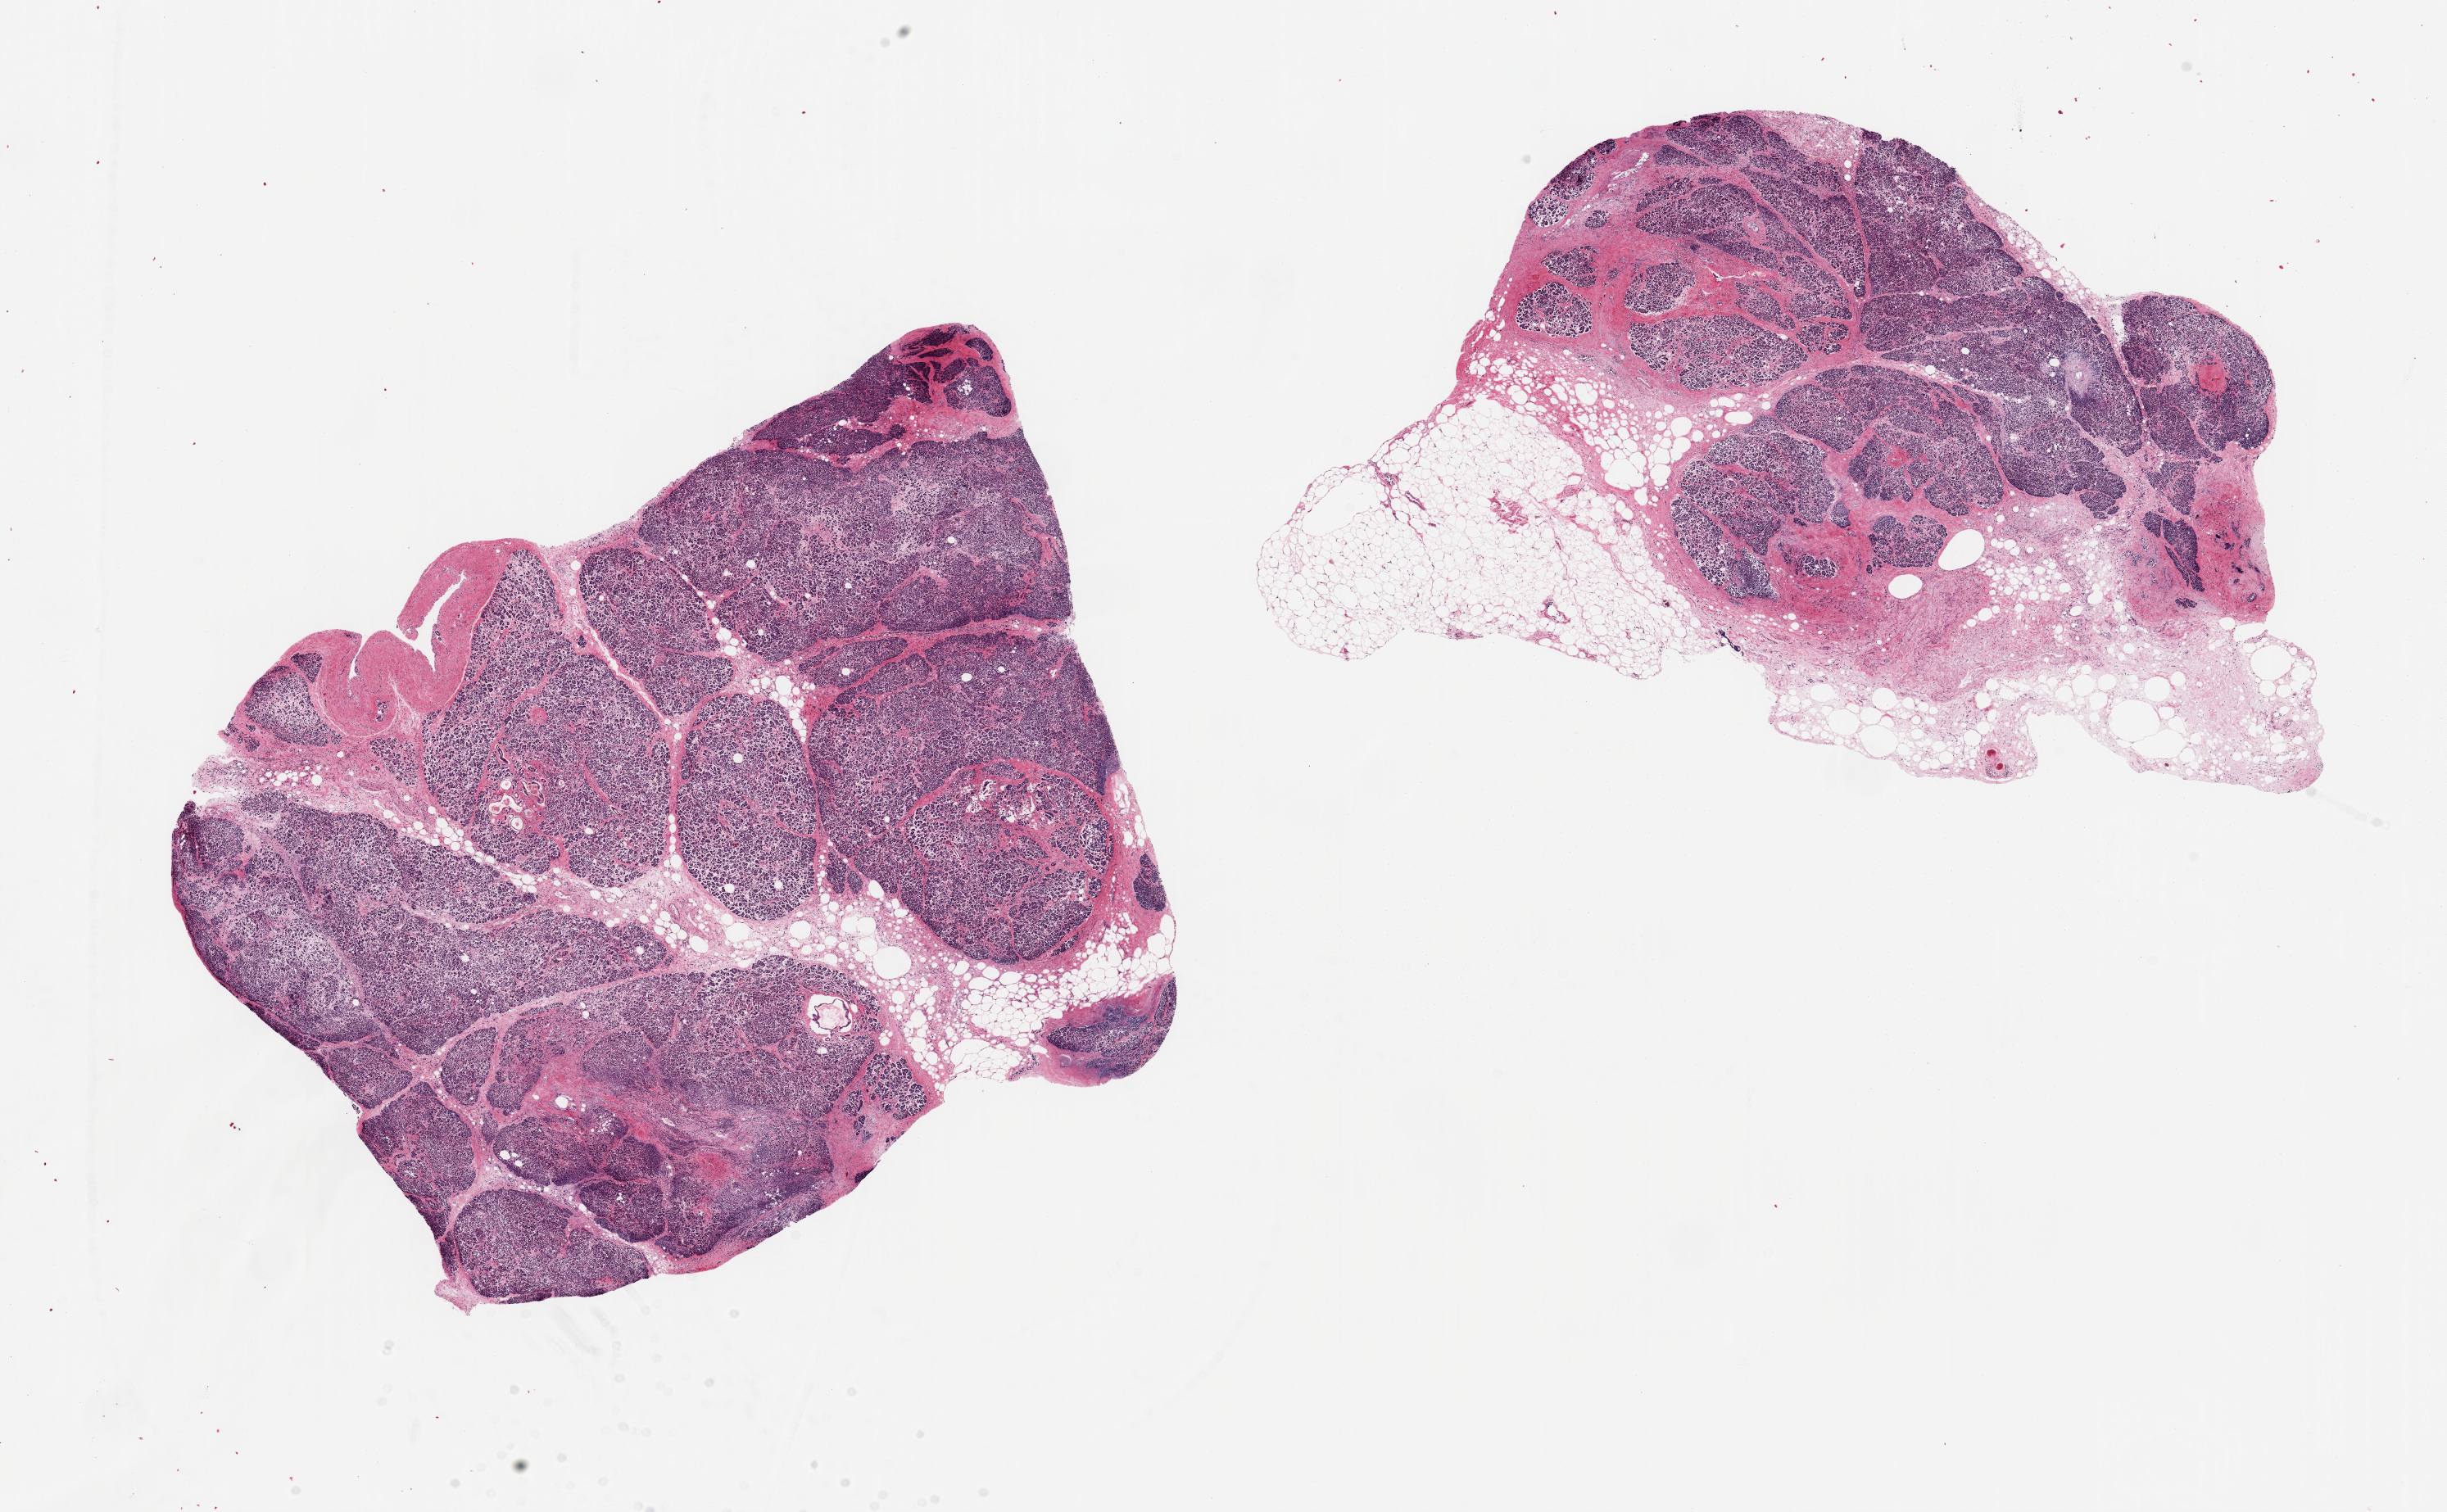
Haematoxylin and eosin whole-slide image — a low-resolution overview of the entire scanned area, about 23.6 x 14.6 mm, PAXgene-fixed, paraffin-embedded tissue, target tissue: pancreas, tissue donor sample. Donor: male.
Reviewer comment on this tissue sample: ~9x6mm pieces, about 30% fat, moderate postmortem saponification.